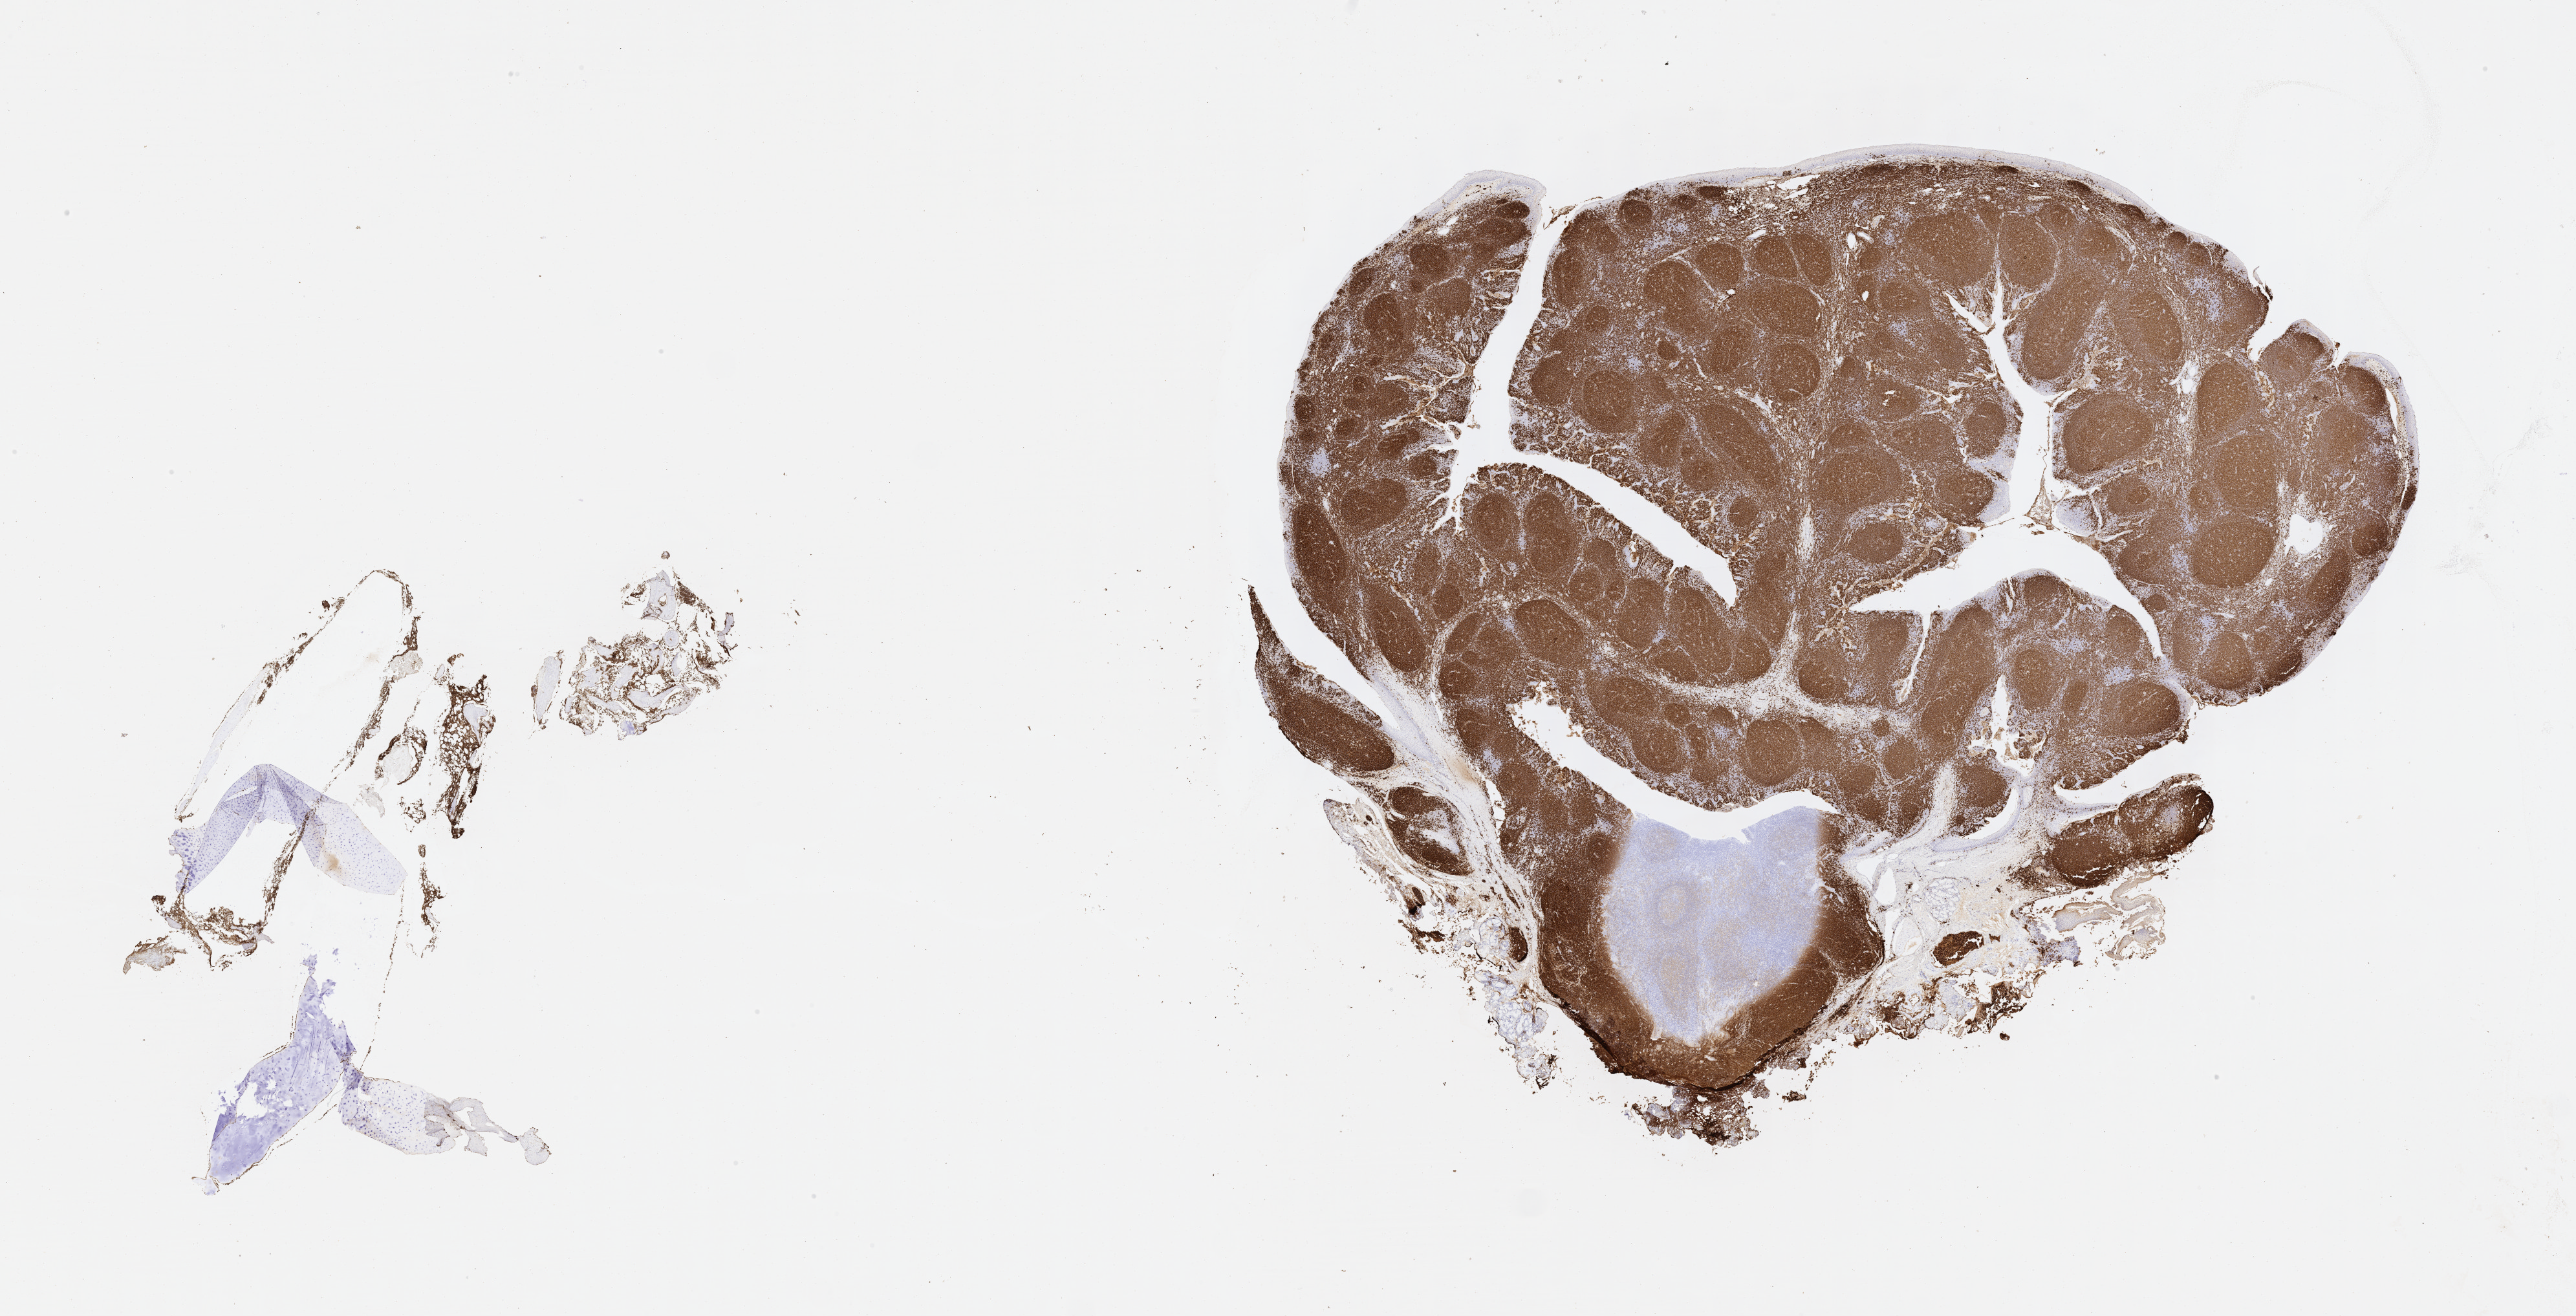
Whole-slide image, immunohistochemical stain for CD20, shown as a low-resolution overview of the whole scanned area (about 32.2 x 16.5 mm), specimen: tumor tissue, site: bone marrow. Patient female; age 11 years.
* histologic diagnosis: Burkitt lymphoma, NOS